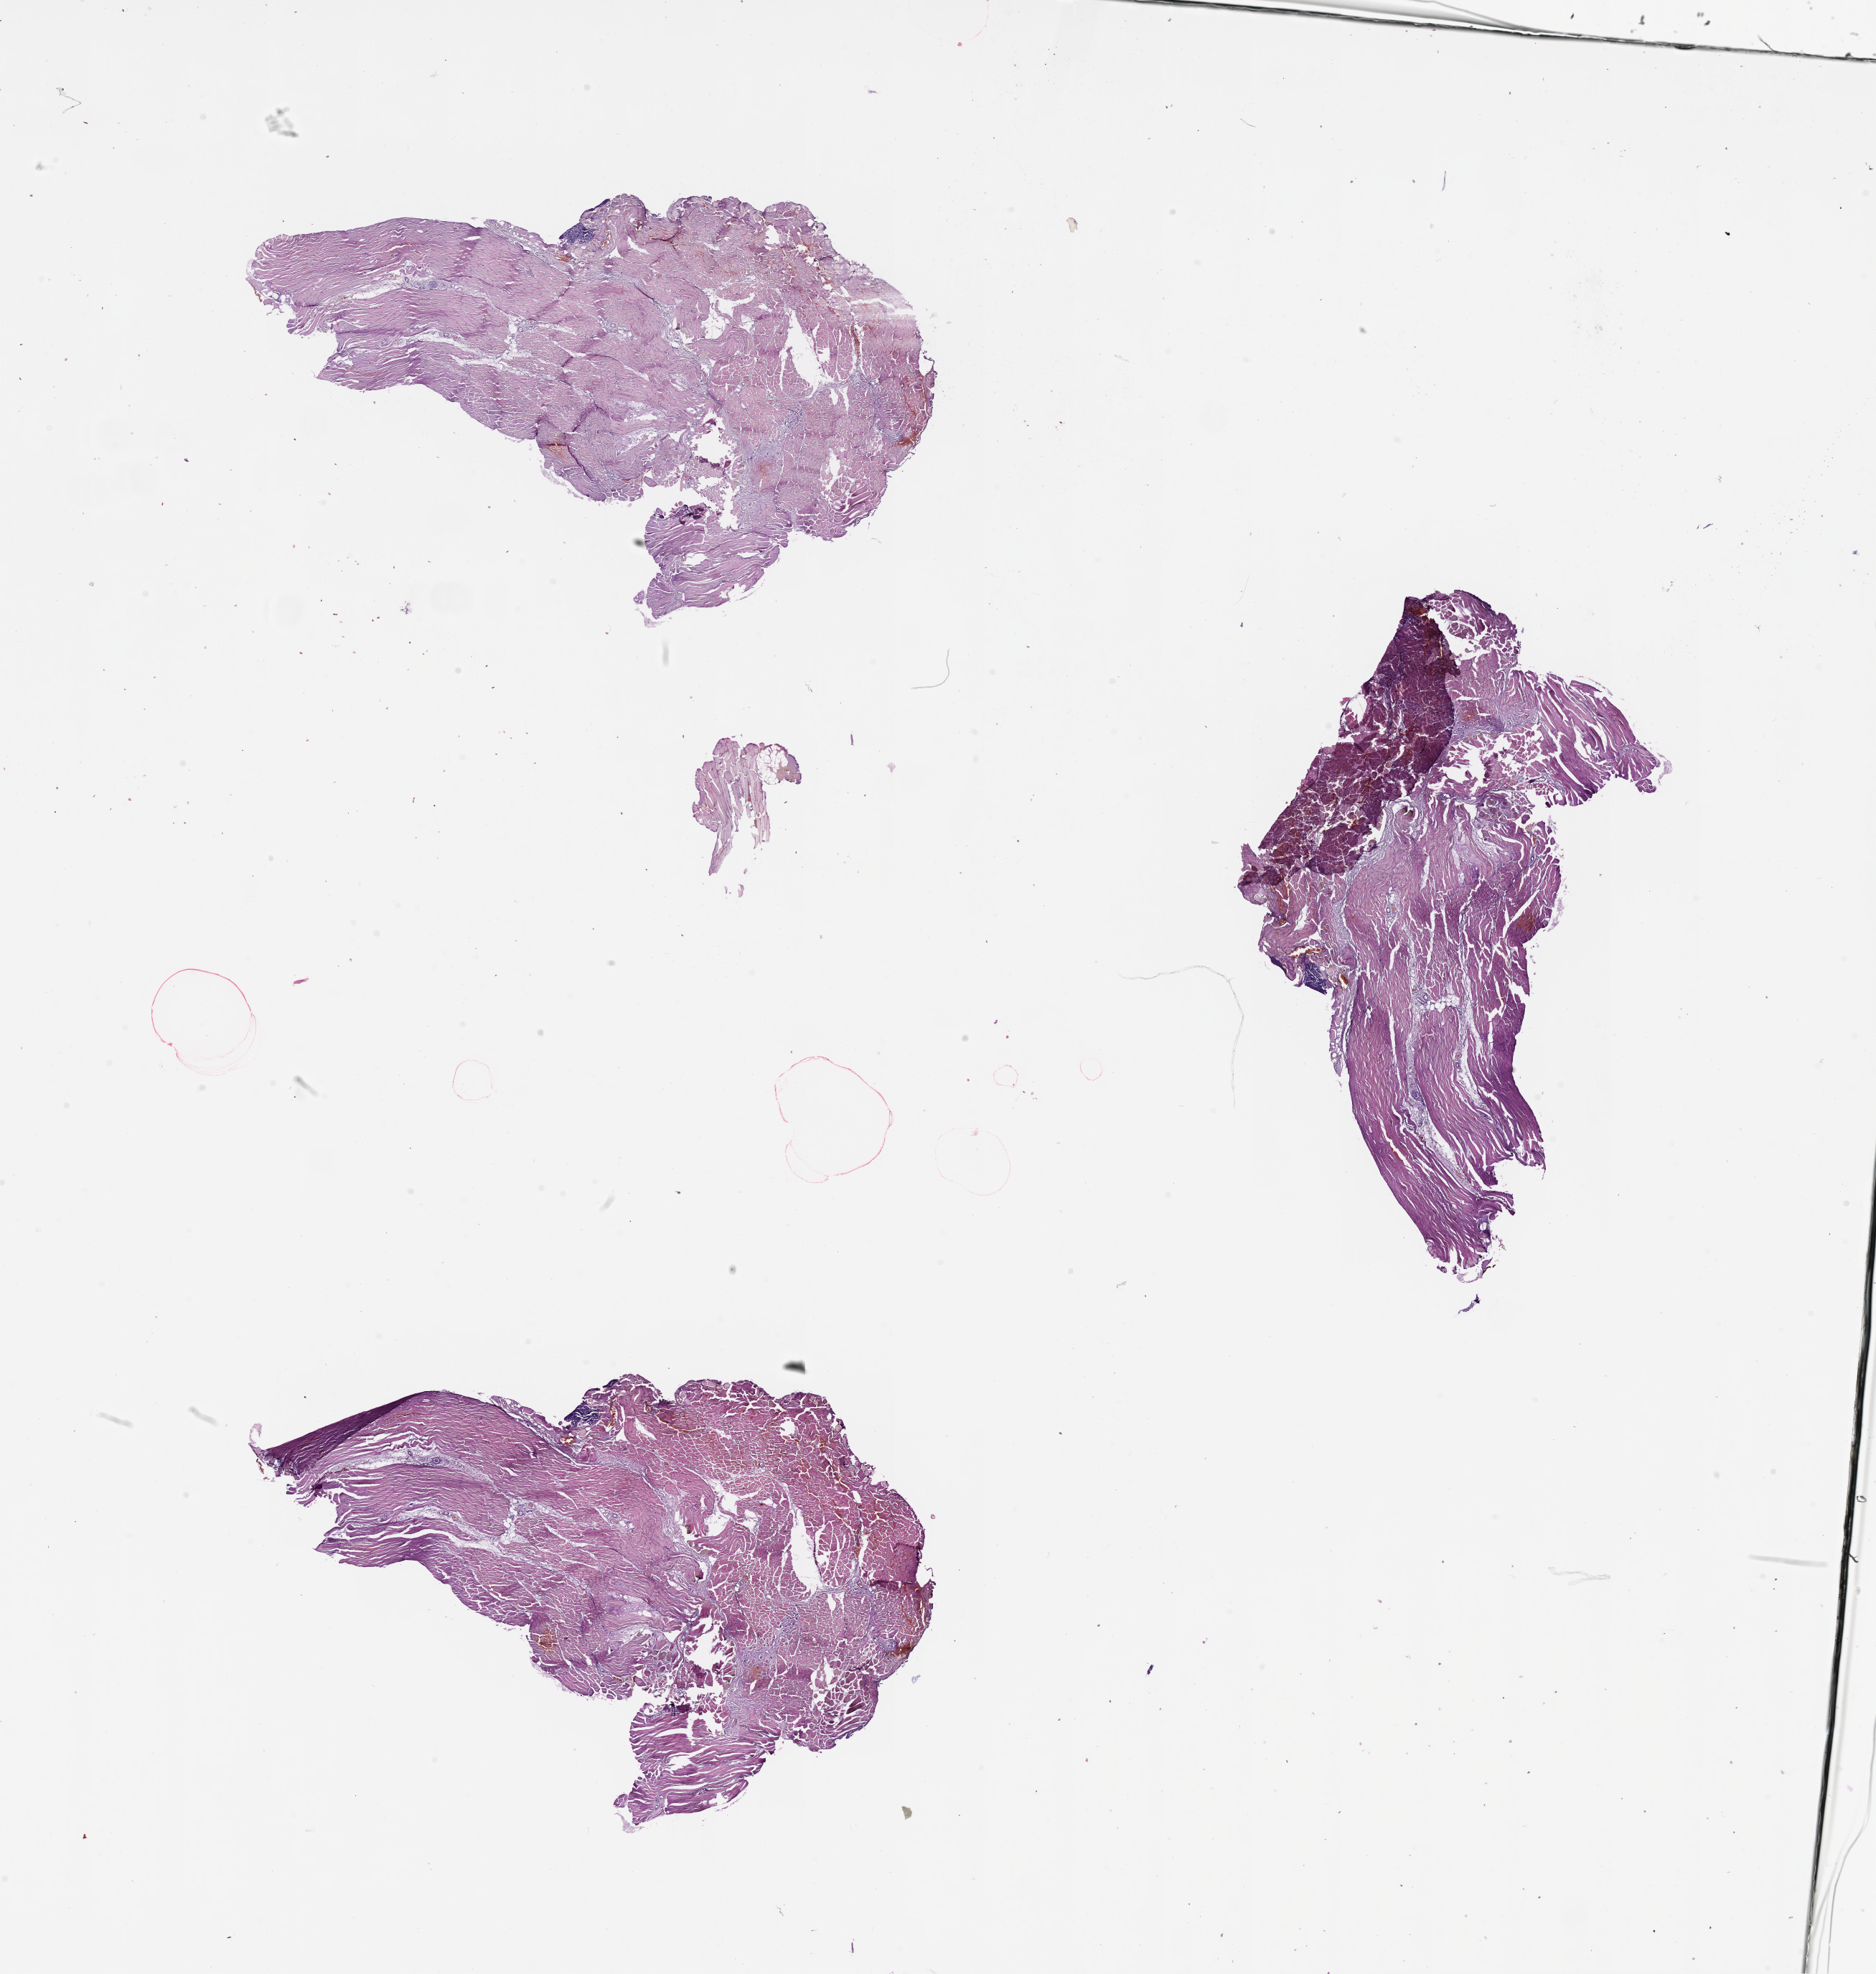
Whole-slide histology image, Hematoxylin and eosin (H&E) stained — shown as a low-resolution overview of the whole scanned area (about 21.0 x 22.1 mm).
- patient diagnosis (cohort enrolment): sarcoma (site not recorded at cohort level)